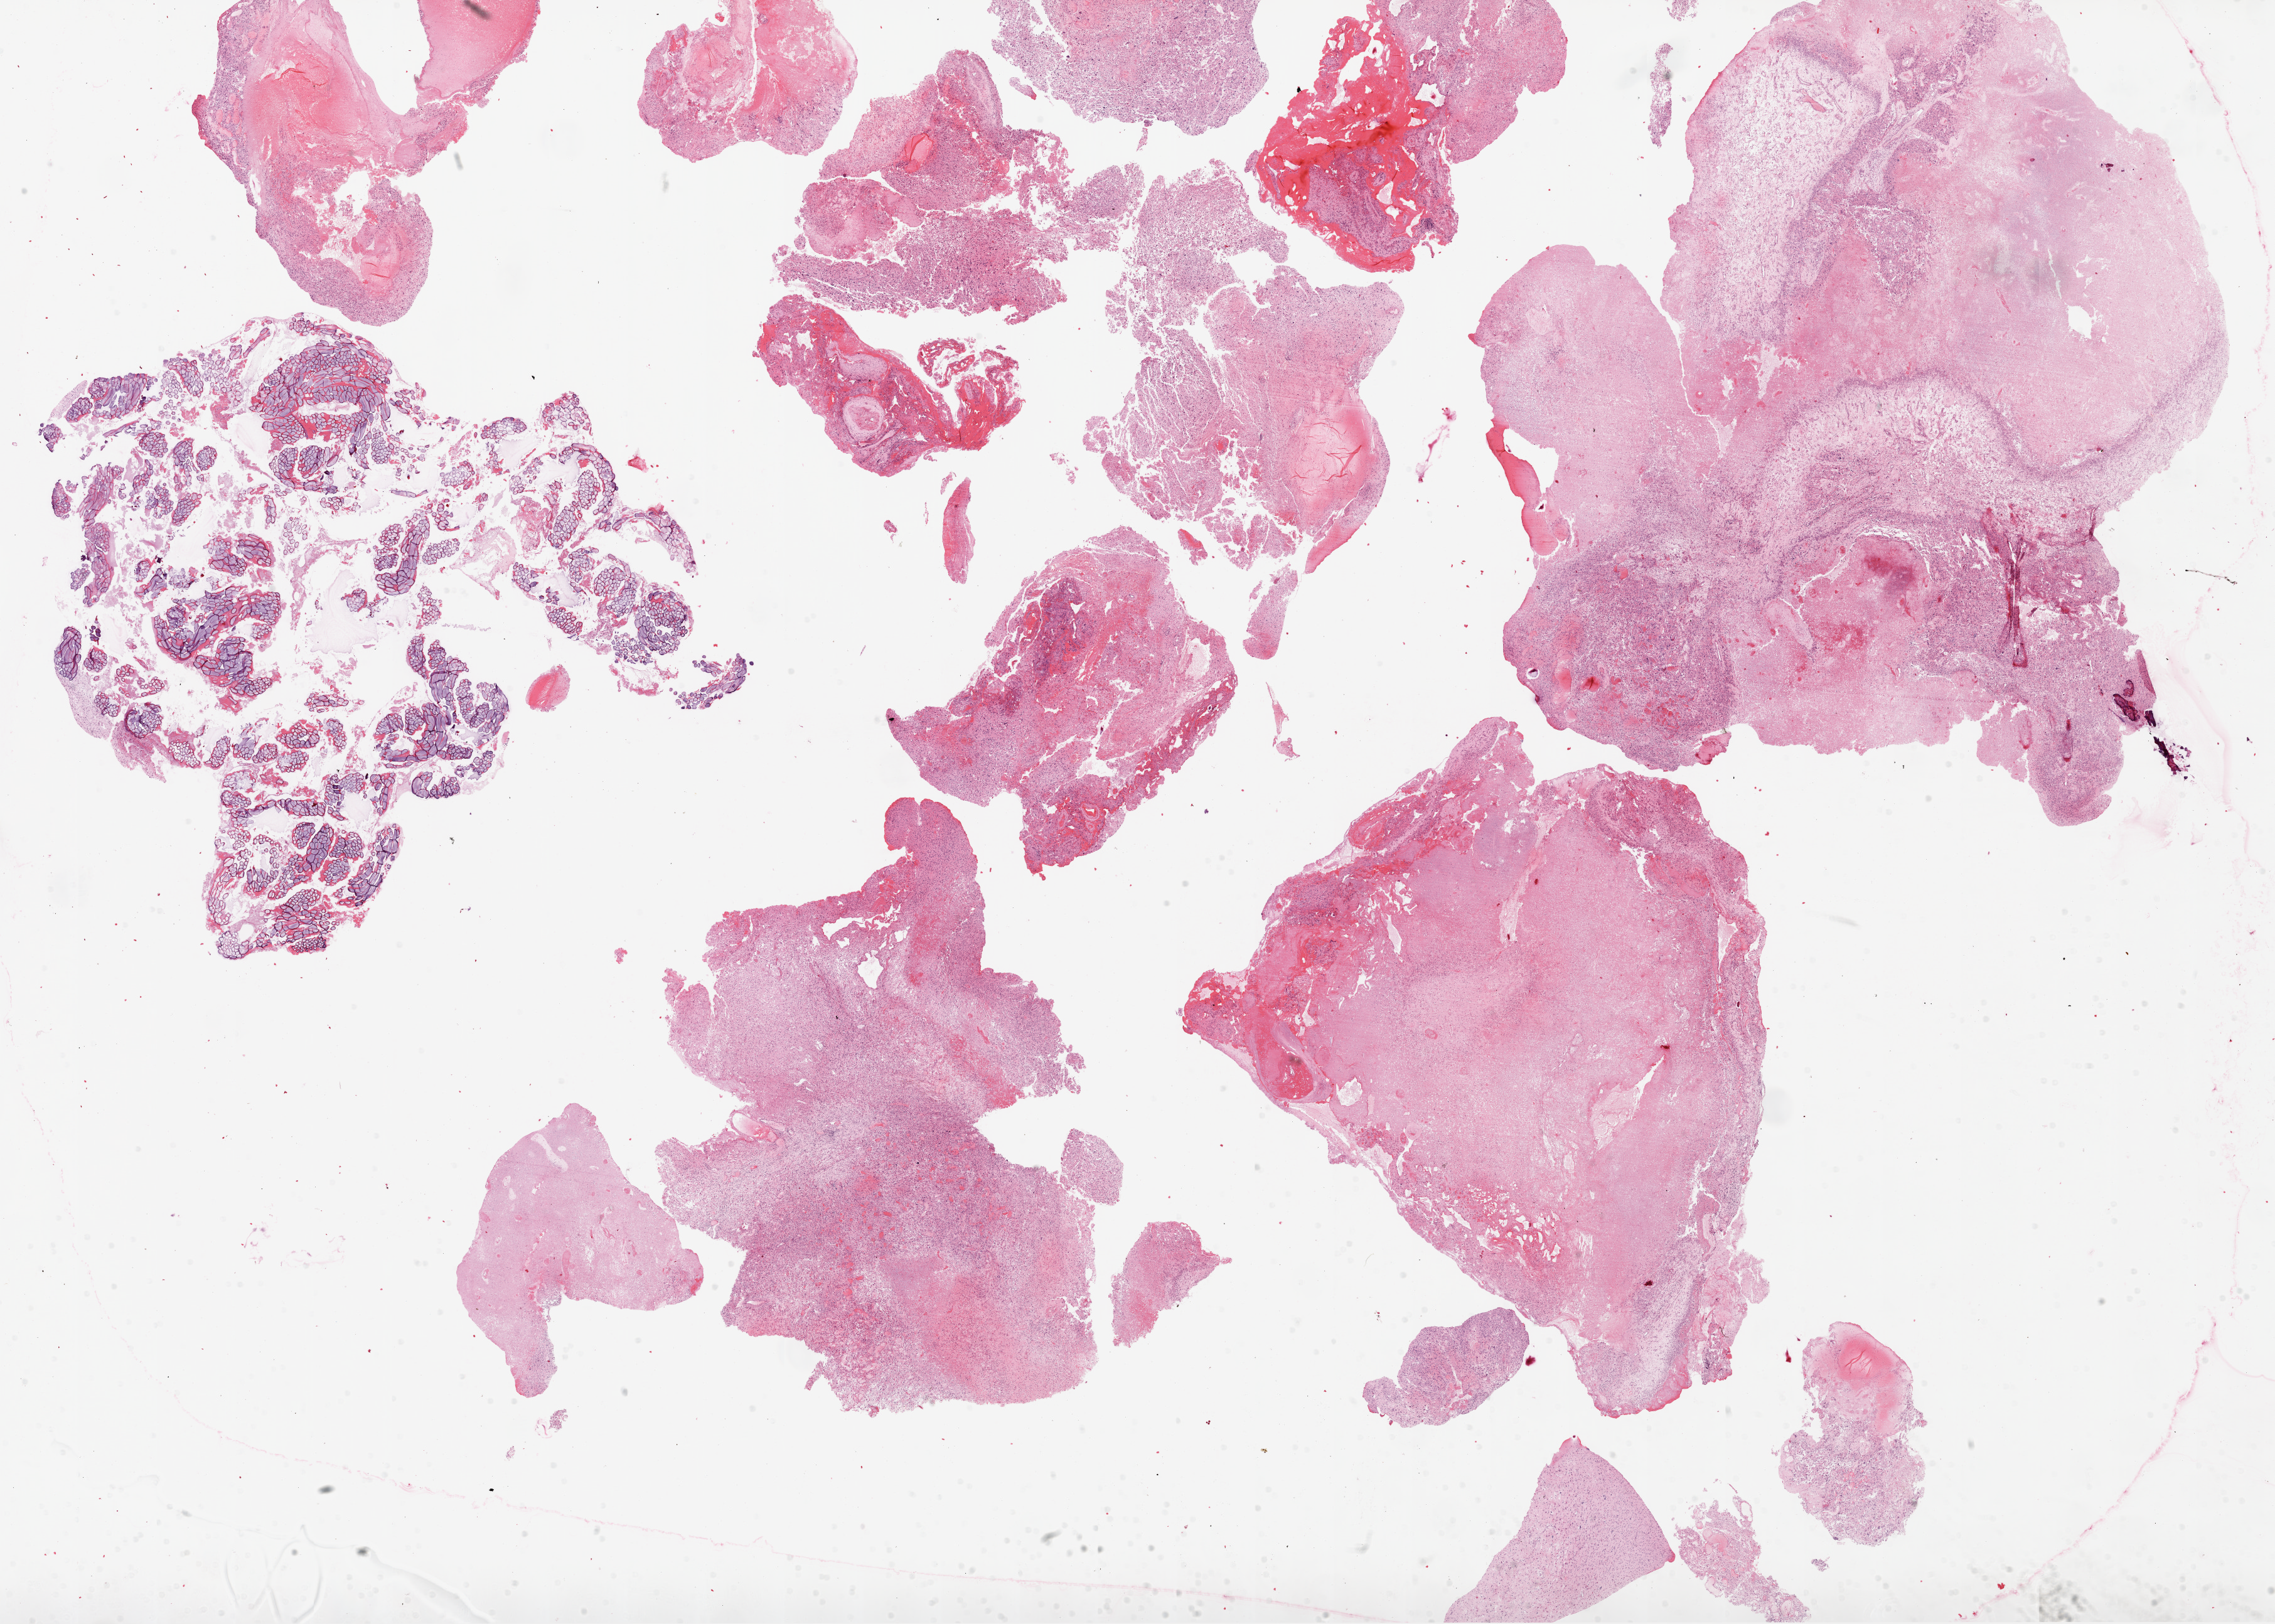
Digitized H&E tissue section (whole slide), a low-resolution overview of the entire scanned area, about 29.1 x 20.8 mm; formalin-fixed paraffin-embedded (FFPE) diagnostic section; sample: primary tumour, brain. Patient: female, age at initial diagnosis 53 years.
Pathologic diagnosis: Glioblastoma.